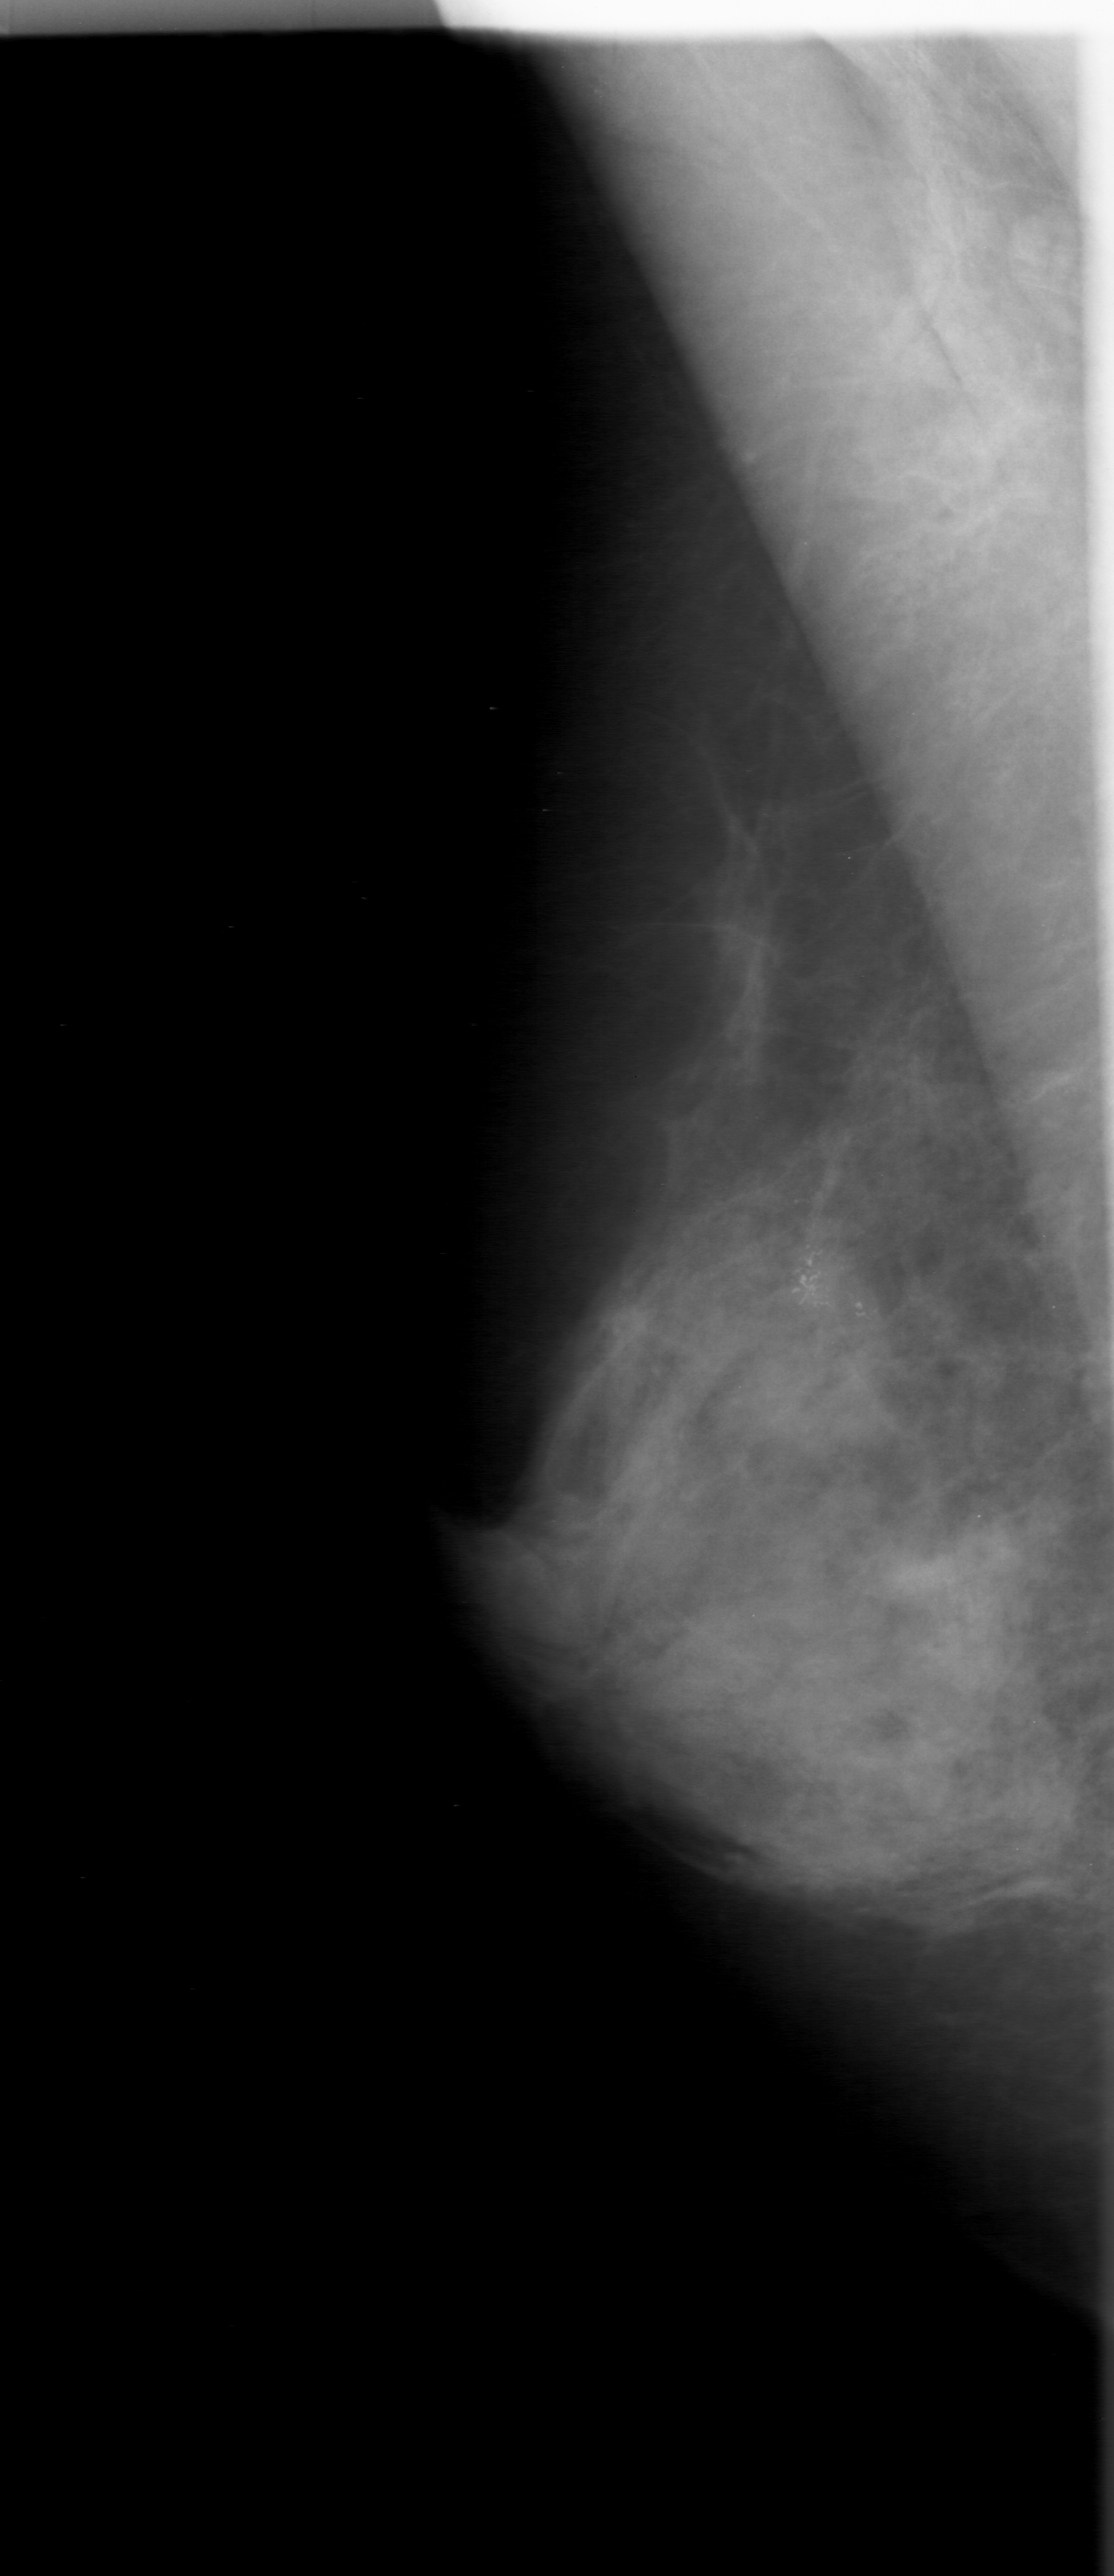
Digitized screen-film mammogram; right breast; MLO view; breast composition: heterogeneously dense (BI-RADS density category 3 of 4); 1114 × 2576 image matrix.
Expert-marked regions of interest on this image (one box per marked abnormality):
- calcifications, morphology fine linear branching, distribution clustered; BI-RADS assessment category 3; subtlety rating 5 on a 1 (subtle) to 5 (obvious) scale; pathology result (as recorded, not read from the image): malignant: bounding box [x1, y1, x2, y2] px = [633, 1142, 956, 1469]